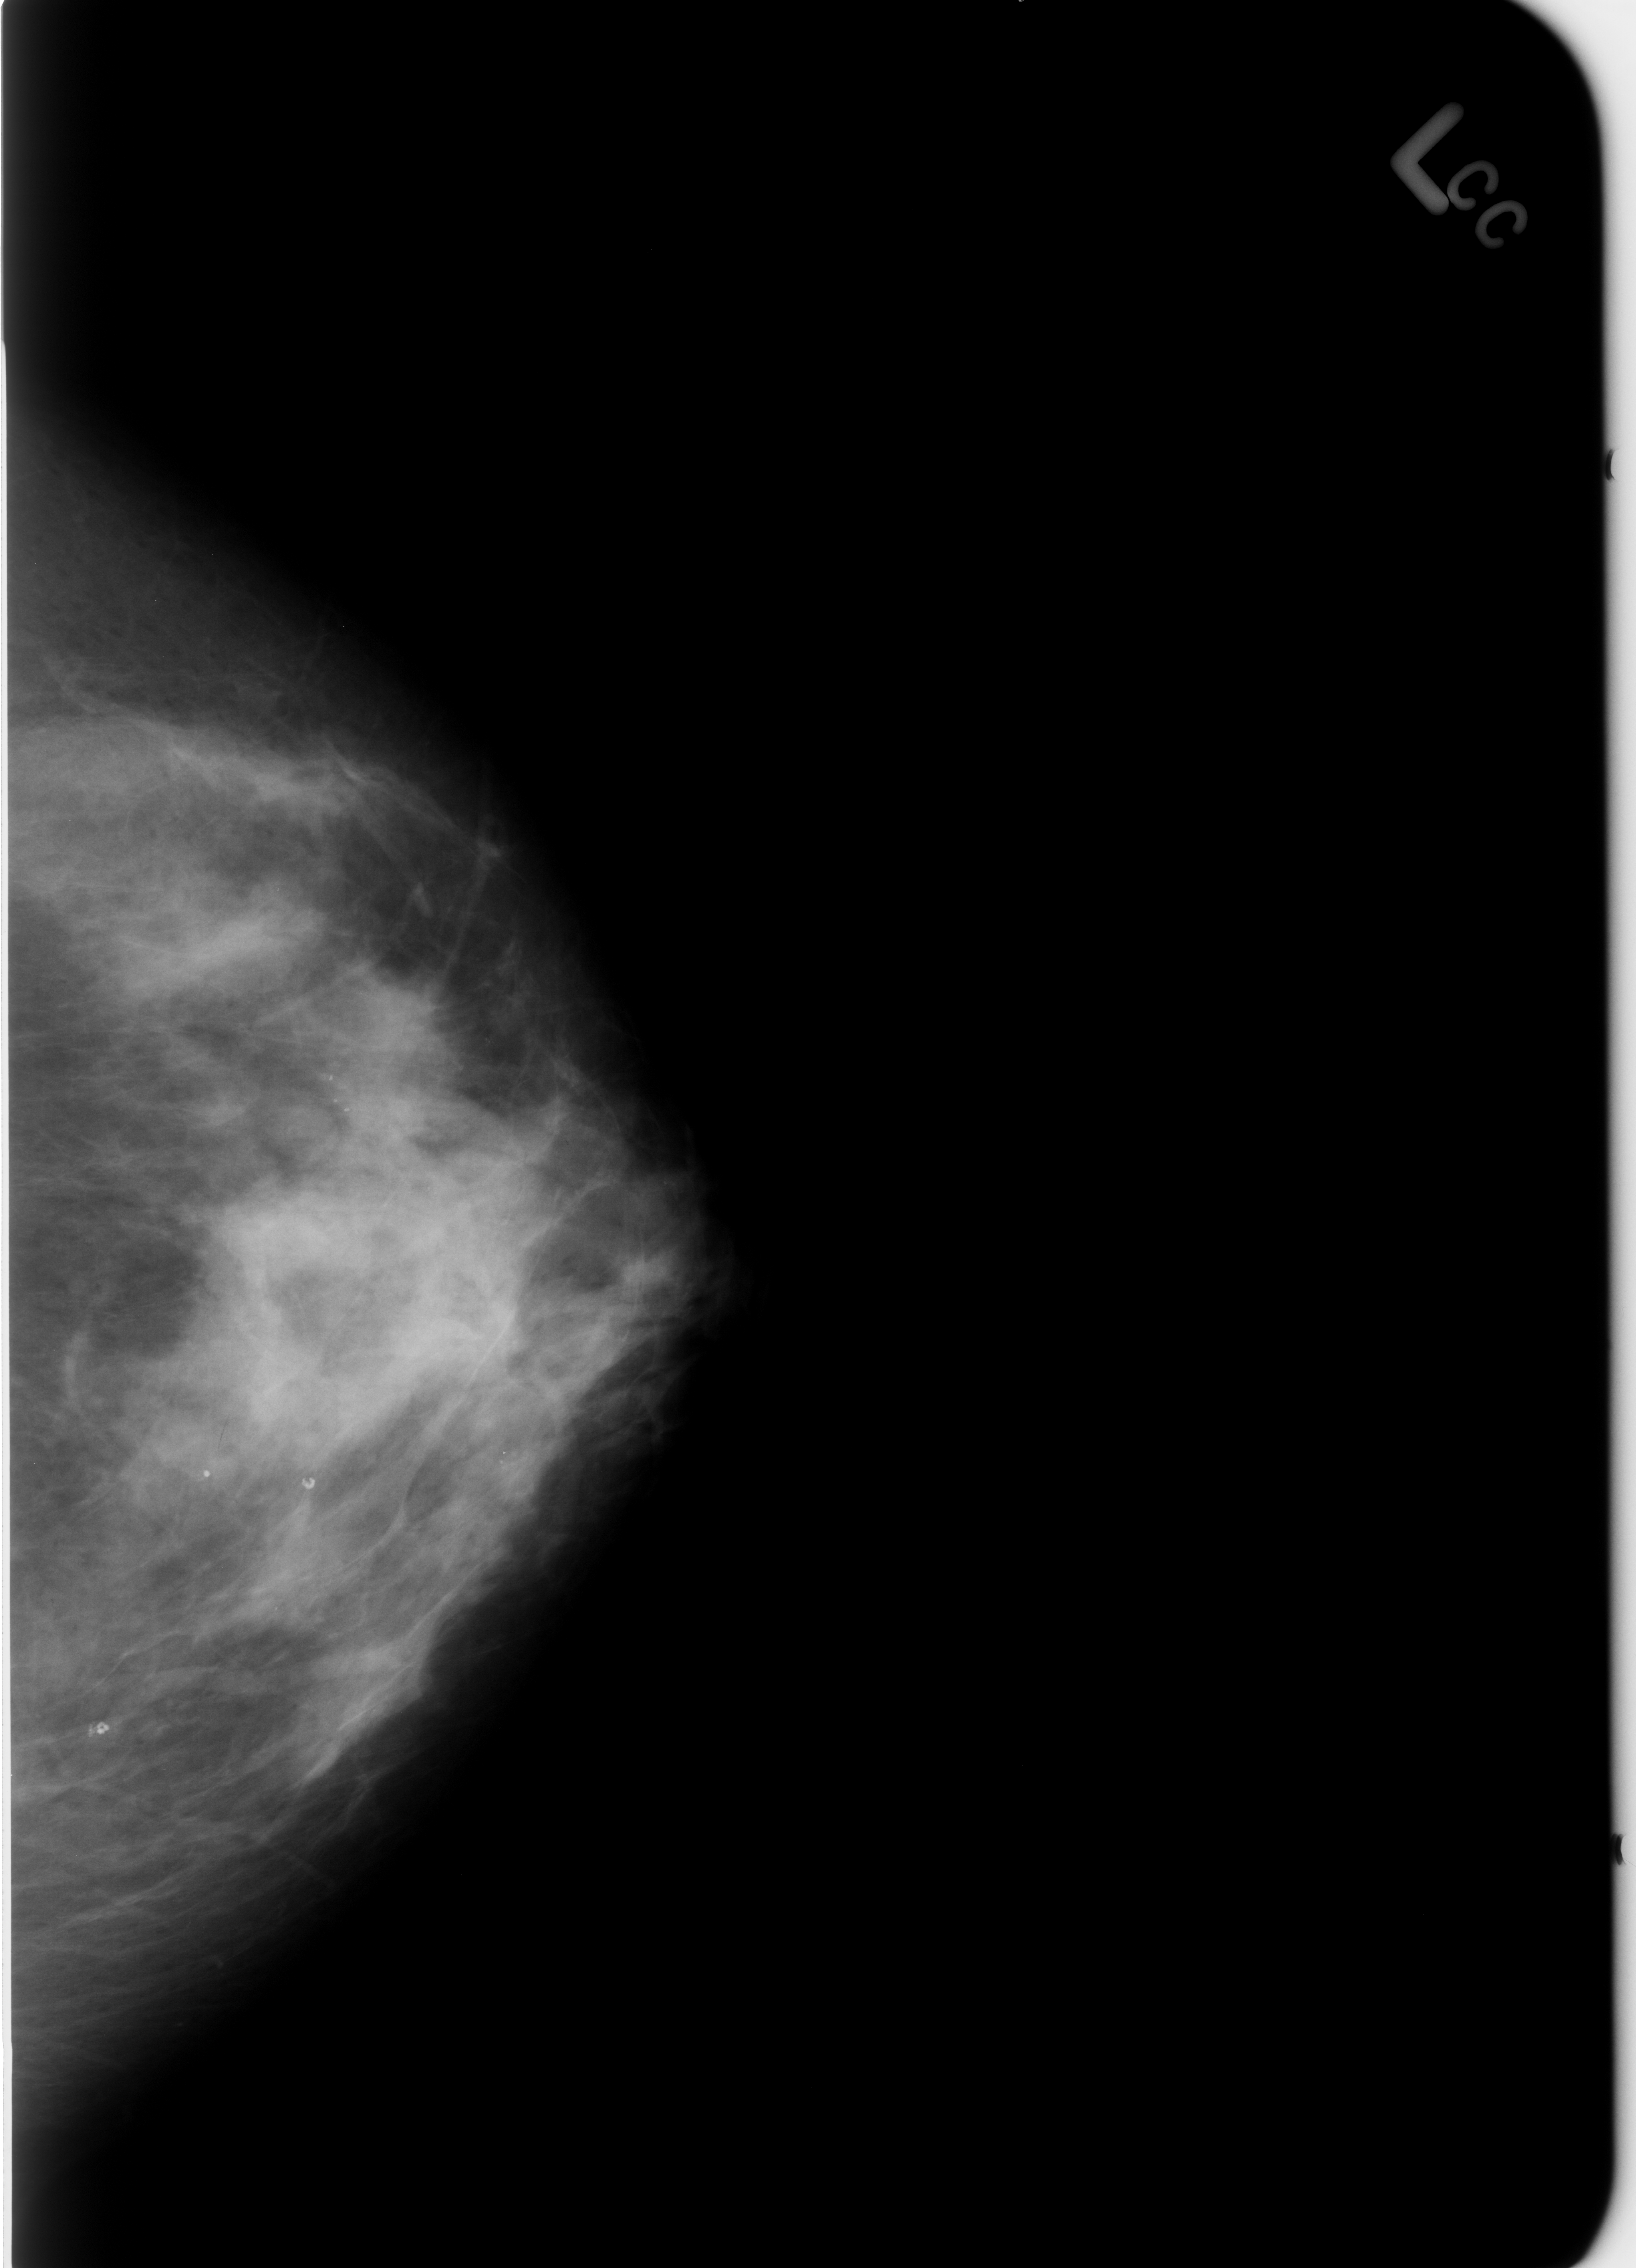
Scanned film-screen mammogram; left breast; craniocaudal (CC) view; breast composition: heterogeneously dense (BI-RADS density category 3 of 4); 1636 × 2268 image matrix.
Expert-marked regions of interest on this image (one box per marked abnormality):
- Finding 1 of 3: calcifications, morphology round and regular / lucent center; BI-RADS assessment category 2; benign; no additional work-up was recommended (outcome (as recorded, no biopsy): benign without callback): bounding box (x1, y1, x2, y2) in pixels: (70, 1696, 138, 1767)
- Finding 2 of 3: calcifications, morphology round and regular / lucent center; BI-RADS assessment category 2; subtlety rating 5 on a 1 (subtle) to 5 (obvious) scale; outcome (as recorded, no biopsy): benign without callback (not worked up further): (169, 1456, 241, 1502)
- Finding 3 of 3: calcifications, morphology round and regular / lucent center; BI-RADS assessment category 2; outcome (as recorded, no biopsy): benign without callback (not worked up further): (281, 1466, 343, 1509)